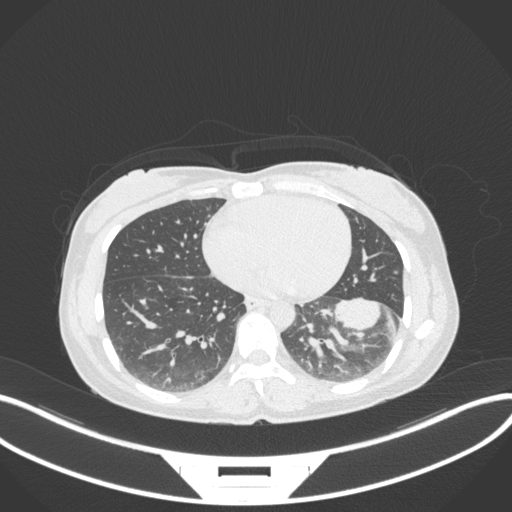
Chest CT, one axial slice. 120 kVp. Lung window (W 1500 / L -600 HU). 1 mm slice thickness. 512 × 512 image matrix, field of view 400 × 400 mm. Patient: female, 41 years. From the clinical record (not read from this slice): clinical TNM (as recorded): T2a N3 M1b.
Structures marked on this image (bounding box drawn by a radiologist):
- lung tumour (recorded histology: adenocarcinoma): bounding box <331,298,392,336> (left, top, right, bottom; pixels)